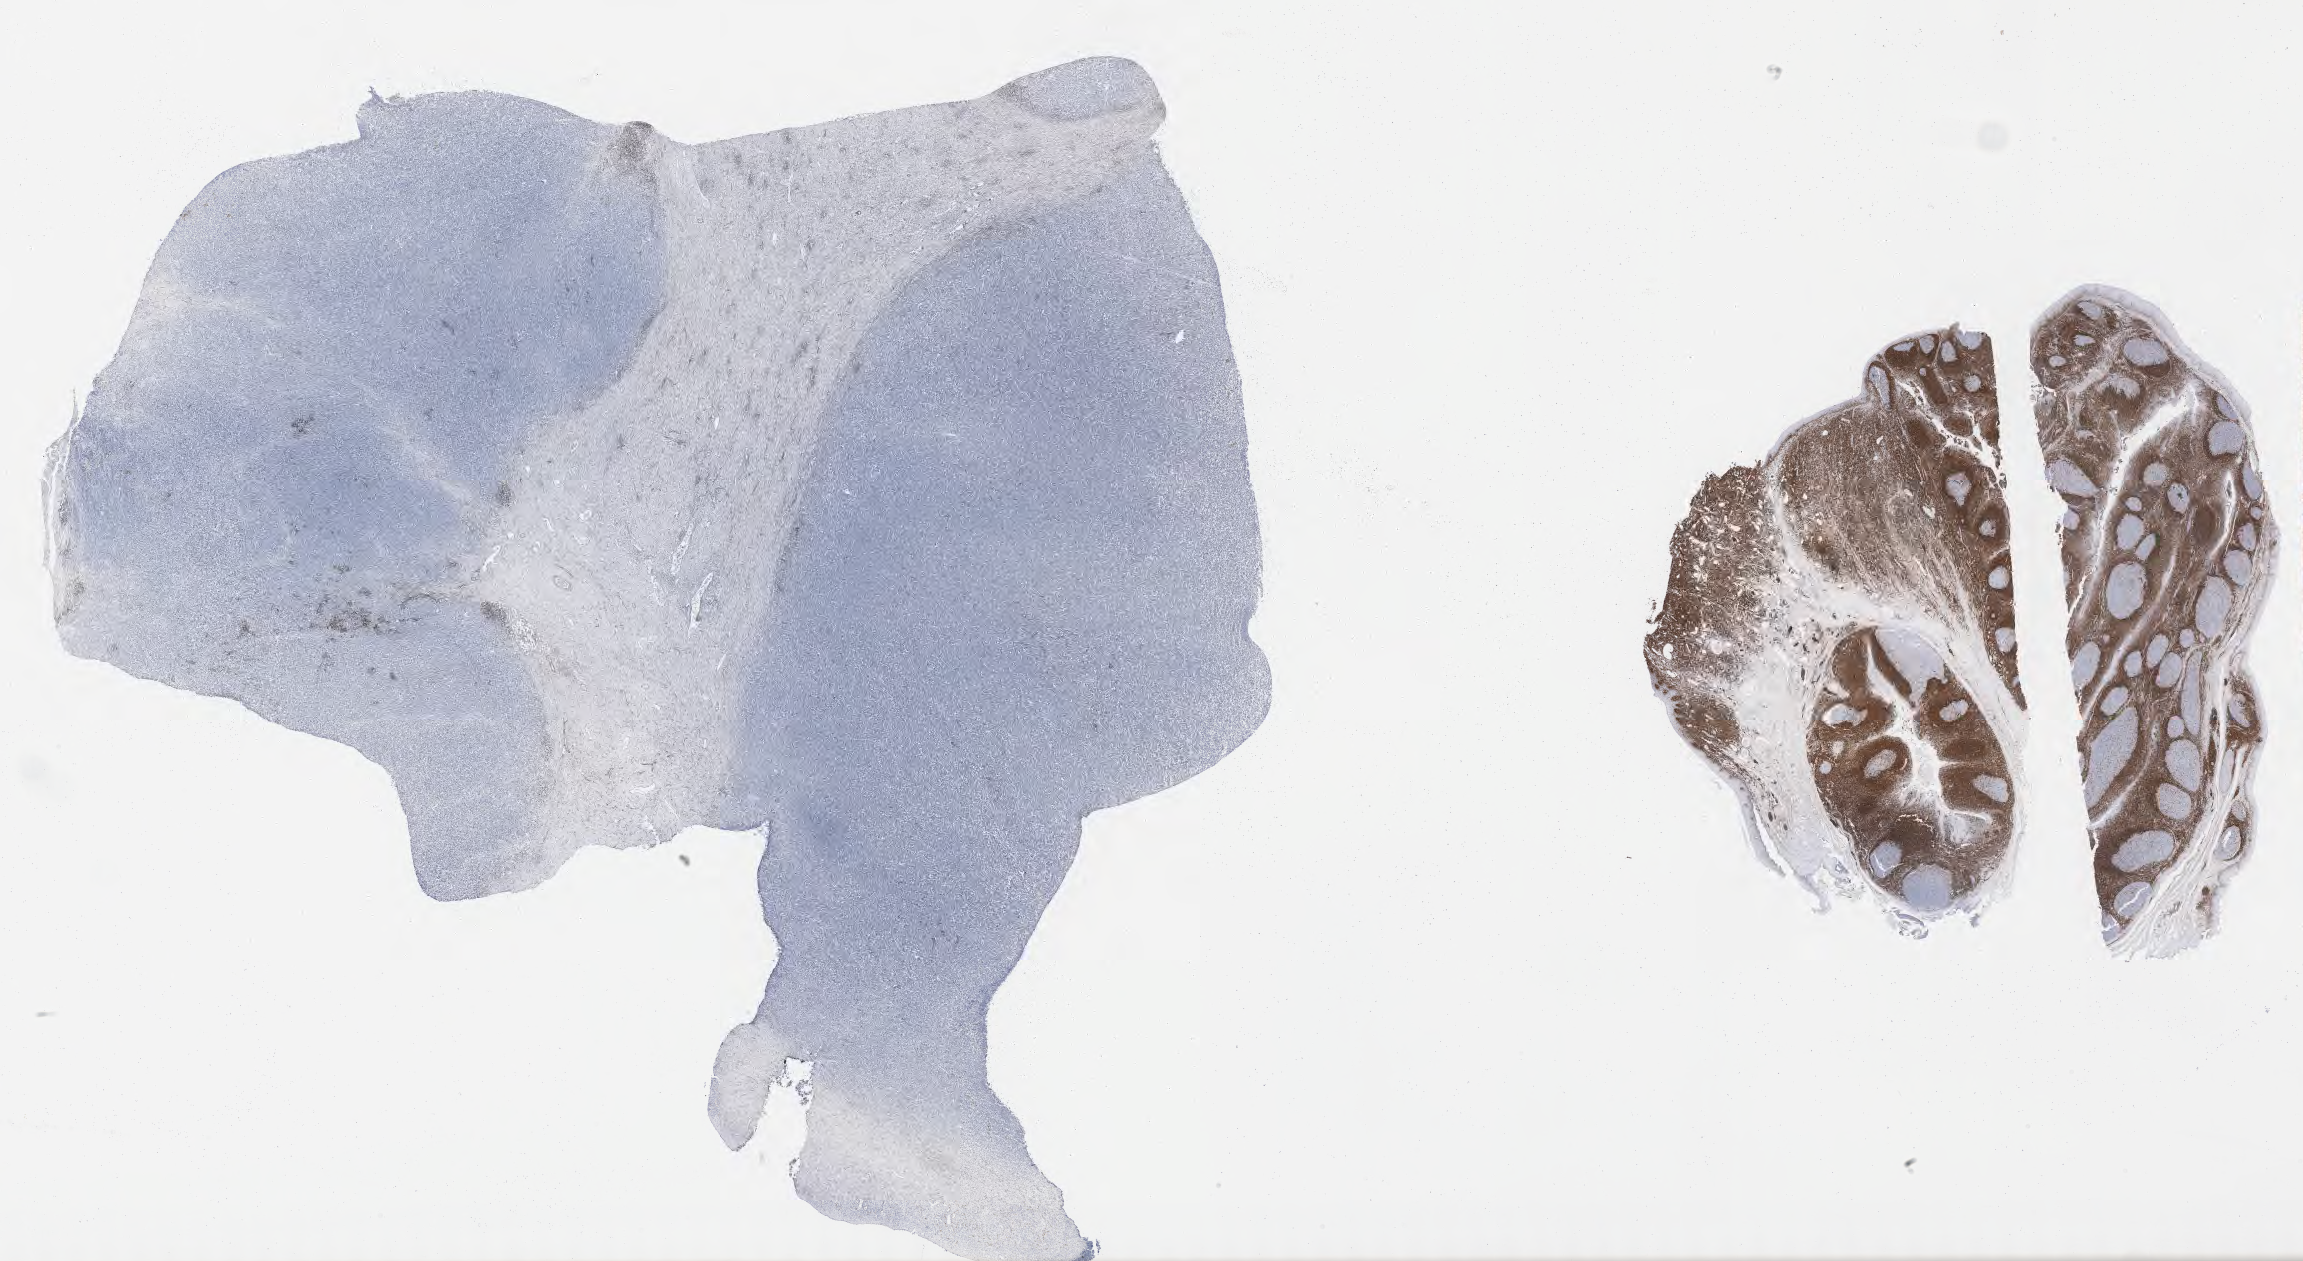
Immunohistochemistry (IHC) whole-slide image stained for BCL2 — whole scanned area (about 37.2 x 20.4 mm) shown as a low-resolution overview, tumor tissue. Patient: female, age at initial diagnosis 8 years.
- histologic diagnosis: Burkitt lymphoma, NOS